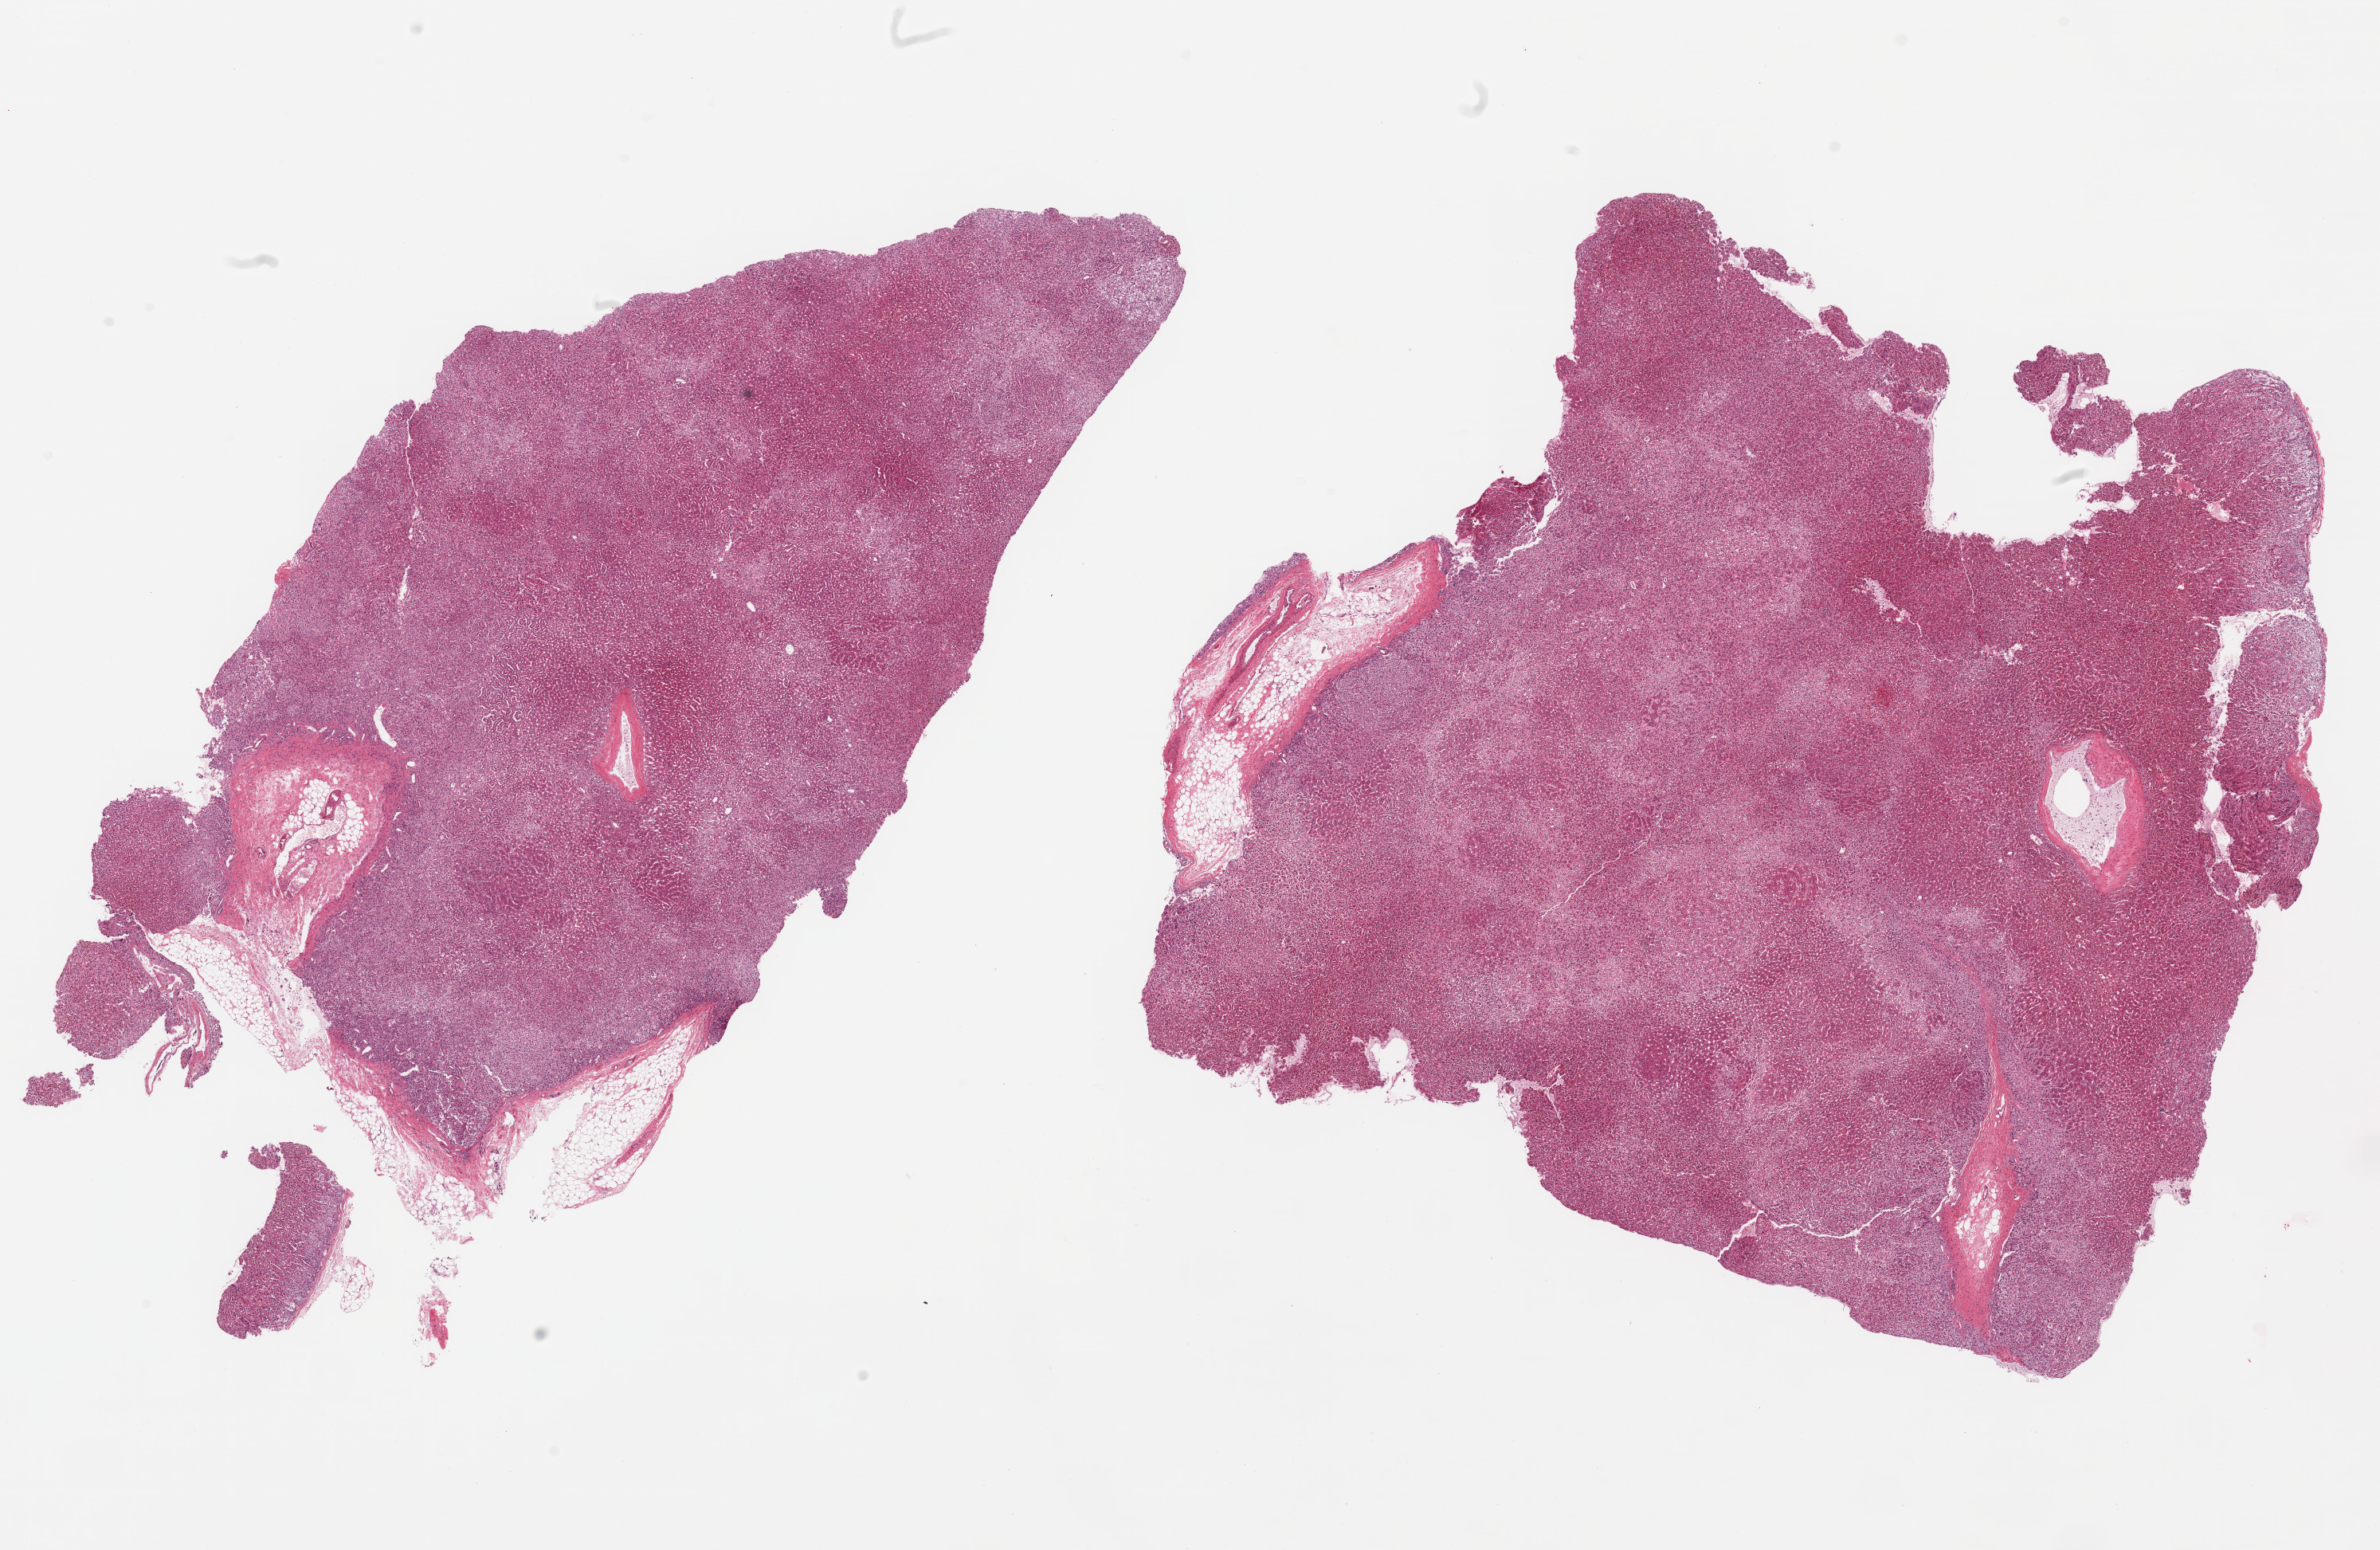
Whole-slide image, haematoxylin and eosin stain — shown as a low-resolution overview of the whole scanned area (about 23.6 x 15.4 mm, slide scanned at 20x). PAXgene-fixed, paraffin-embedded tissue. Section of adrenal gland (target tissue). Tissue donor sample. Male donor.
Pathologist's review note for this sample: 2 pieces; small attachment of fat (~5%).